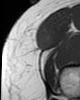
MRI of an extremity soft-tissue mass, one axial slice; MR volume resampled by the dataset authors to the PET/CT grid (not the native acquisition matrix); 3.27 mm slice thickness; 80 × 100 image matrix. Female patient. Case-level facts recorded for this patient, not image findings: histological type: synovial sarcoma; grade: intermediate; site of the primary tumour: right thigh.
Outlined on this slice (expert contour drawn on MRI and transferred to this co-registered scan by the dataset authors):
- gross tumour volume including surrounding oedema: bounding box <37,31,52,50> (left, top, right, bottom; pixels)
- gross tumour volume (mass): <35,31,52,50>